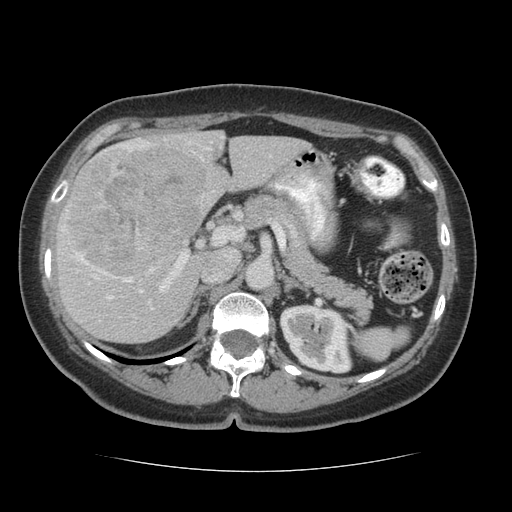
Contrast-enhanced abdominal CT (liver protocol), one axial slice; slice 35 of 75 in the series (ordered by position); 140 kVp; soft-tissue window (W 400 / L 40 HU); 2.5 mm slice thickness; 512 × 512 image matrix, field of view 360 × 360 mm. From the clinical record (not read from this slice): diagnosis: hepatocellular carcinoma (patient treated with transarterial chemoembolisation; whether this scan precedes or follows treatment is not stated here); TNM stage (as recorded): Stage-I; Child-Pugh class: A.
Outlined on this slice (semi-automatic segmentation, software-assisted and operator-edited):
- liver parenchyma outside the tumour (the mass and vessels are separate outlines, so this box may not span the whole liver): bounding box [x1, y1, x2, y2] px = [56, 130, 310, 342]
- mass: [63, 142, 205, 279]
- liver vessels: [61, 139, 271, 310]